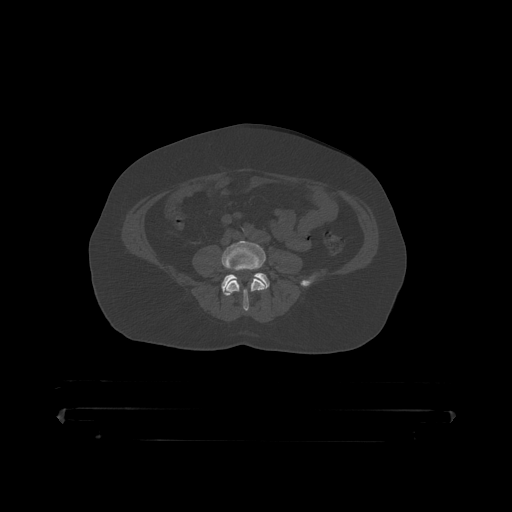
CT including the spine, one axial slice. Reconstruction kernel STANDARD. Bone window (W 1800 / L 400 HU). 1.25 mm slice thickness. 512 × 512 image matrix, field of view 650 × 650 mm. Patient: male, 60 years. Case-level facts recorded for this patient, not image findings: primary cancer: prostate.
Outlined on this slice (semi-automatic segmentation, software-assisted and operator-edited):
- L4 vertebra: box from (x=222, y=241) to (x=266, y=312) px
- L5 vertebra: (x=222, y=273)–(x=270, y=296)